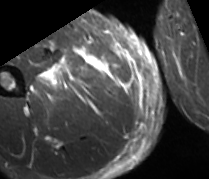
MRI of an extremity soft-tissue mass, one axial slice. Slice 25 of 89 in the series (ordered by position). STIR. MR volume resampled by the dataset authors to the PET/CT grid (not the native acquisition matrix). 3.27 mm slice thickness. 209 × 179 image matrix, field of view 204 × 175 mm. Male patient. Case-level facts recorded for this patient, not image findings: histological type: undifferentiated - pleiomorphic; grade: high; site of the primary tumour: right thigh.
Annotated regions visible in this slice (expert contour drawn on MRI and transferred to this co-registered scan by the dataset authors):
- gross tumour volume including surrounding oedema: bounding box (x1, y1, x2, y2) in pixels: (35, 55, 108, 93)